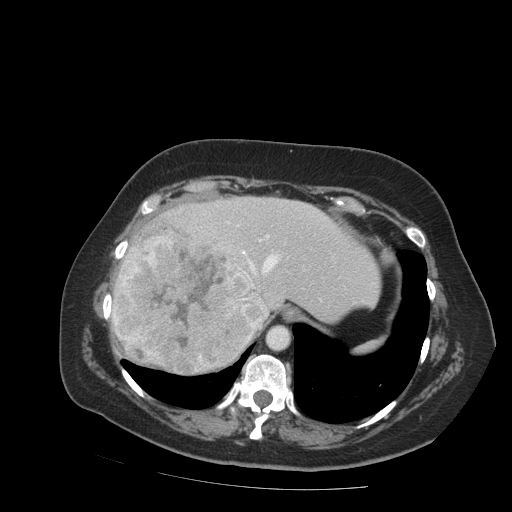
Contrast-enhanced abdominal CT (liver protocol), one axial slice. Reconstruction kernel STANDARD. 140 kVp. Soft-tissue window (W 400 / L 40 HU). 2.5 mm slice thickness. 512 × 512 image matrix, field of view 400 × 400 mm. From the clinical record (not read from this slice): diagnosis: hepatocellular carcinoma (patient treated with transarterial chemoembolisation; whether this scan precedes or follows treatment is not stated here); TNM stage (as recorded): Stage-IVB; Child-Pugh class: A; tumour differentiation: moderately differentiated; tumour nodularity: uninodular.
Structures marked on this image (semi-automatically segmented with operator editing):
- abdominal aorta: bounding box [x1, y1, x2, y2] px = [266, 326, 290, 350]
- liver parenchyma outside the tumour (the mass and vessels are separate outlines, so this box may not span the whole liver): [112, 196, 376, 368]
- mass: [110, 227, 265, 375]
- liver vessels: [227, 222, 280, 328]